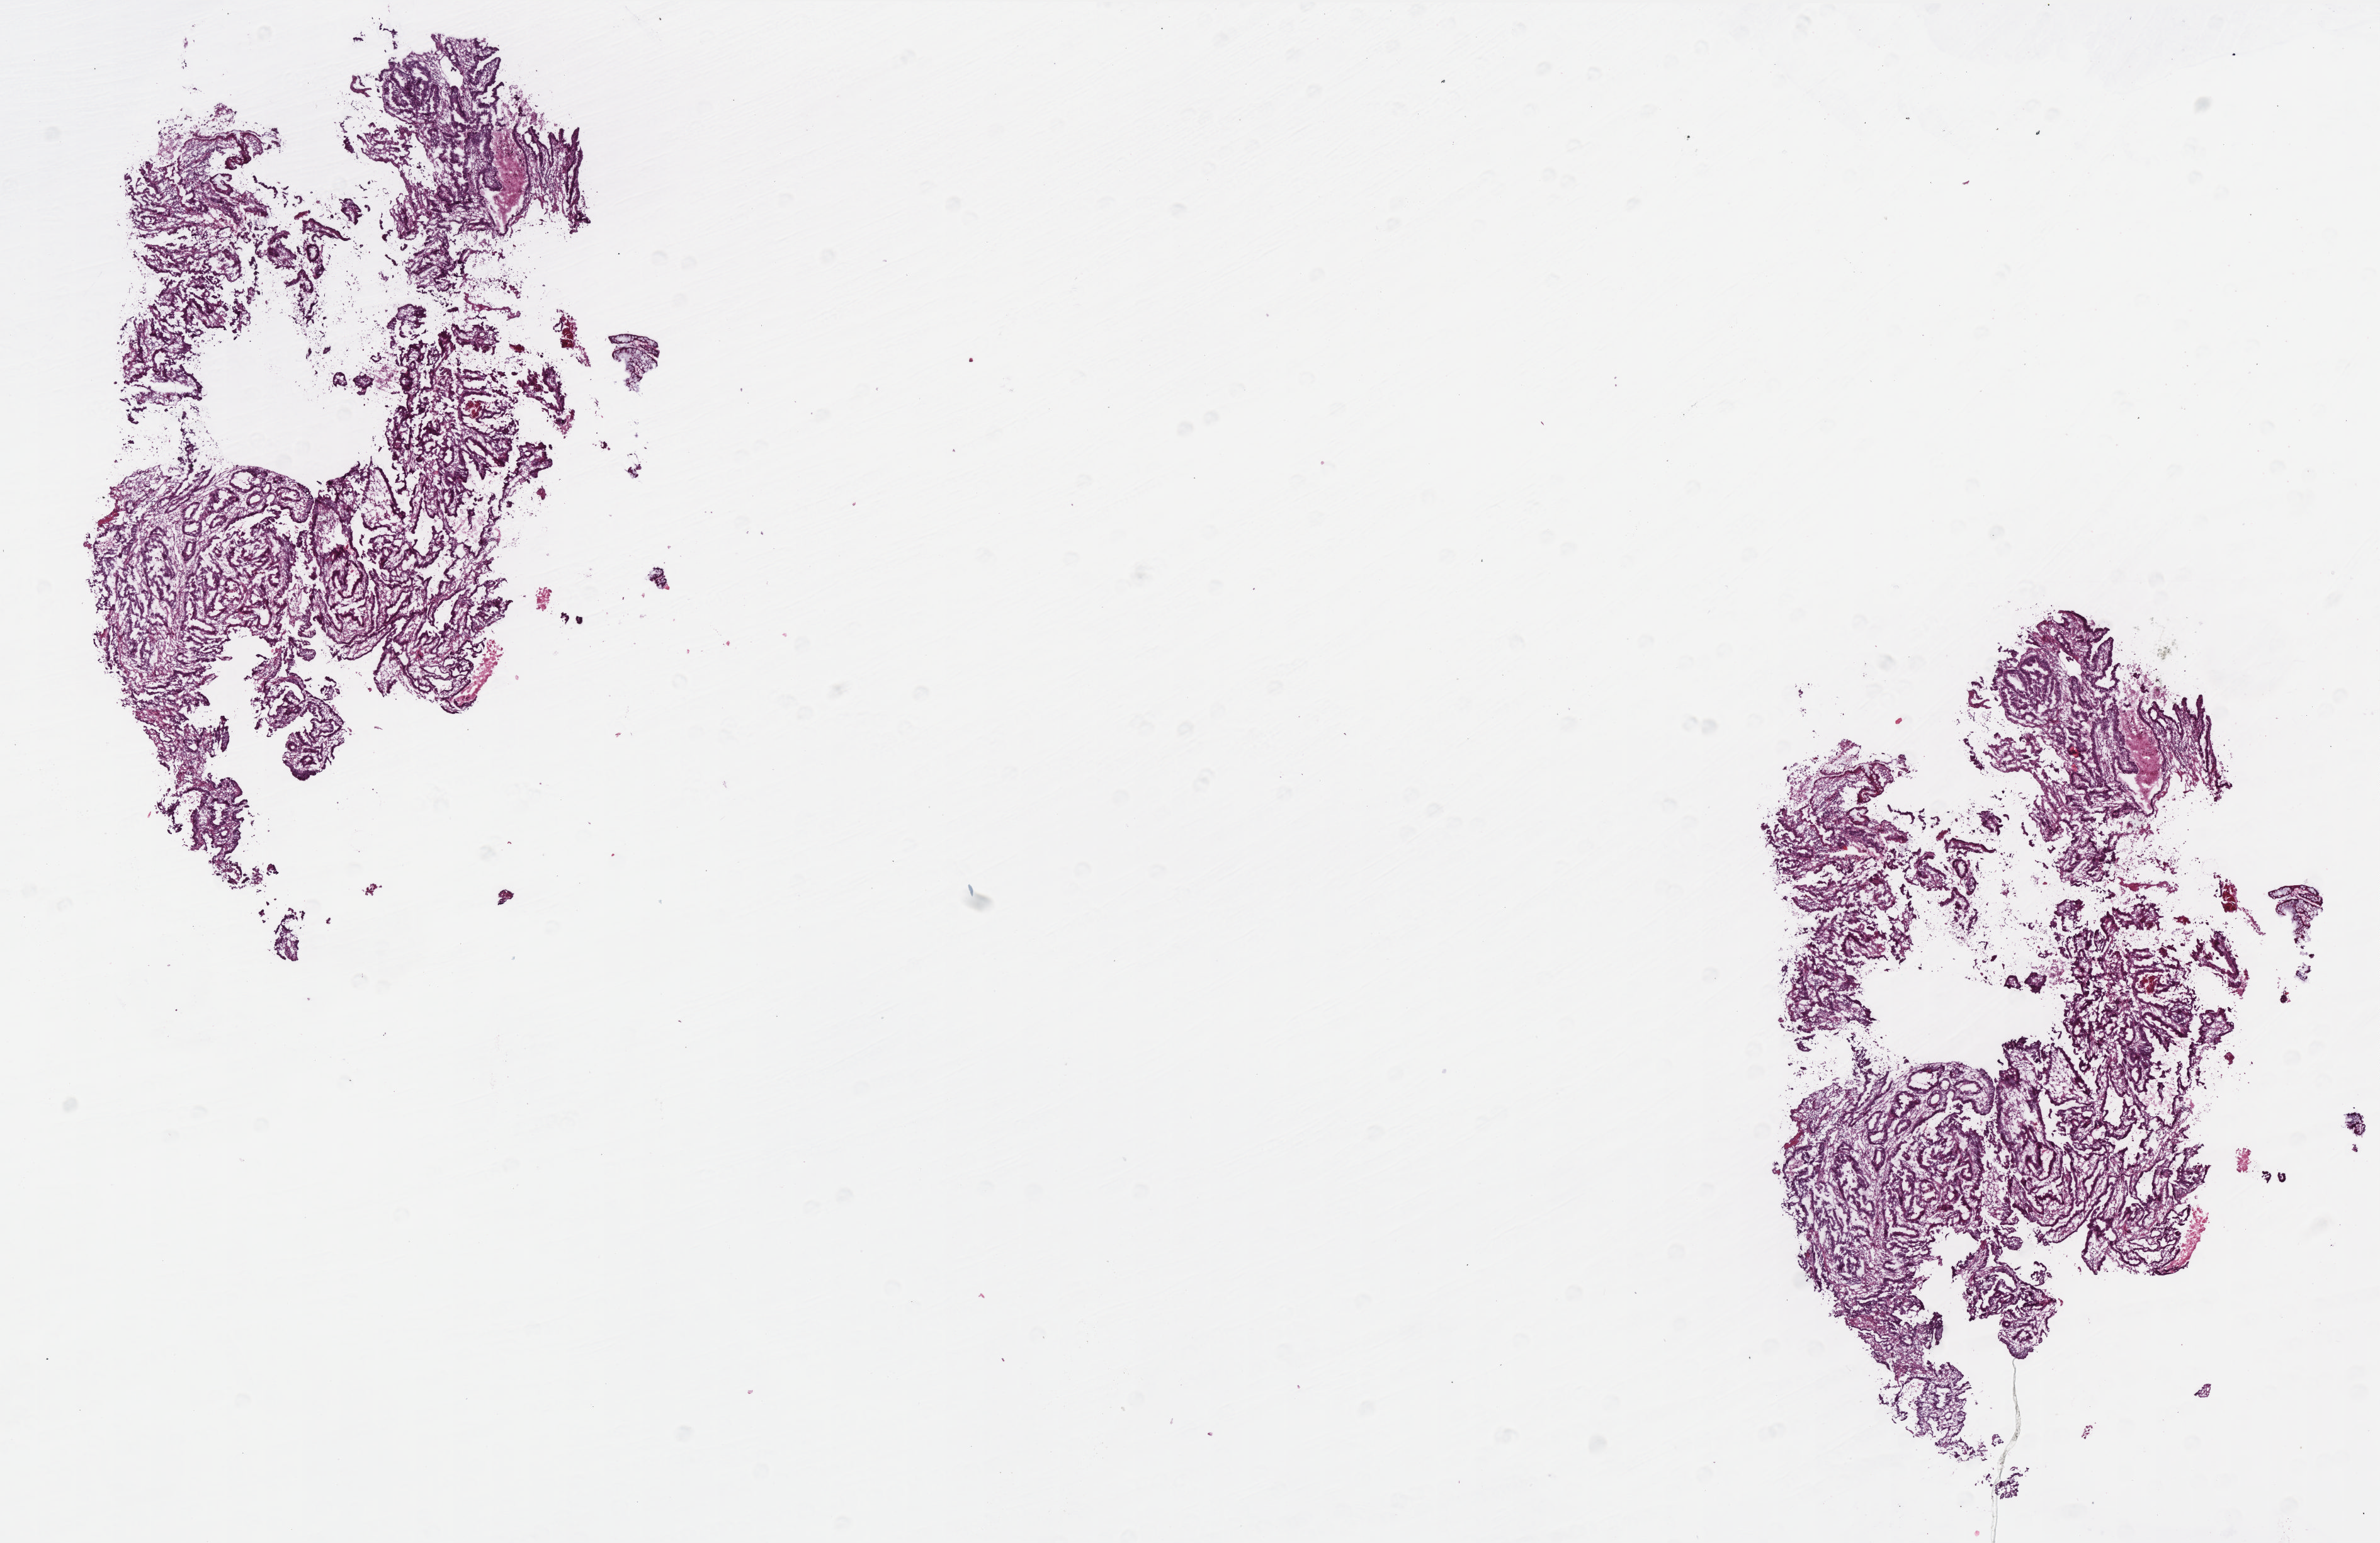
Whole-slide histology image, H&E-stained — shown as a low-resolution overview of the whole scanned area (about 15.2 x 9.8 mm), frozen section from the top of the tissue portion, primary tumour sample from the colon. Male, age 66 years at initial diagnosis.
Histologic diagnosis: Adenocarcinoma, NOS.